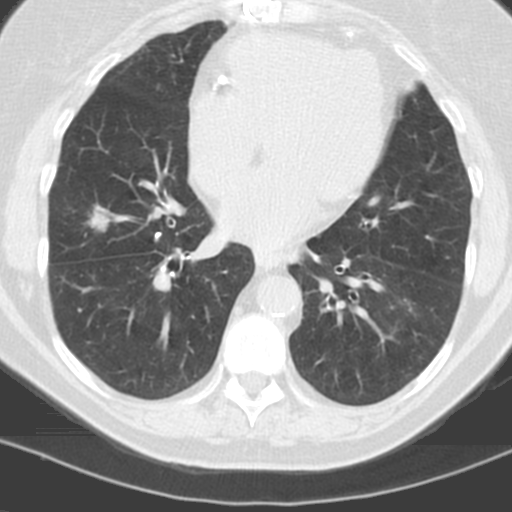
Low-dose screening chest CT, one axial slice. Slice 46 of 121 in the series (ordered by position). 120 kVp. Lung window (W 1500 / L -600 HU). 3.2 mm slice thickness. 512 × 512 image matrix.
Annotated regions visible in this slice (manually delineated by an expert):
- lesion 3 (tumor, middle lobe of right lung): bounding box (x1, y1, x2, y2) in pixels: (89, 212, 108, 230)